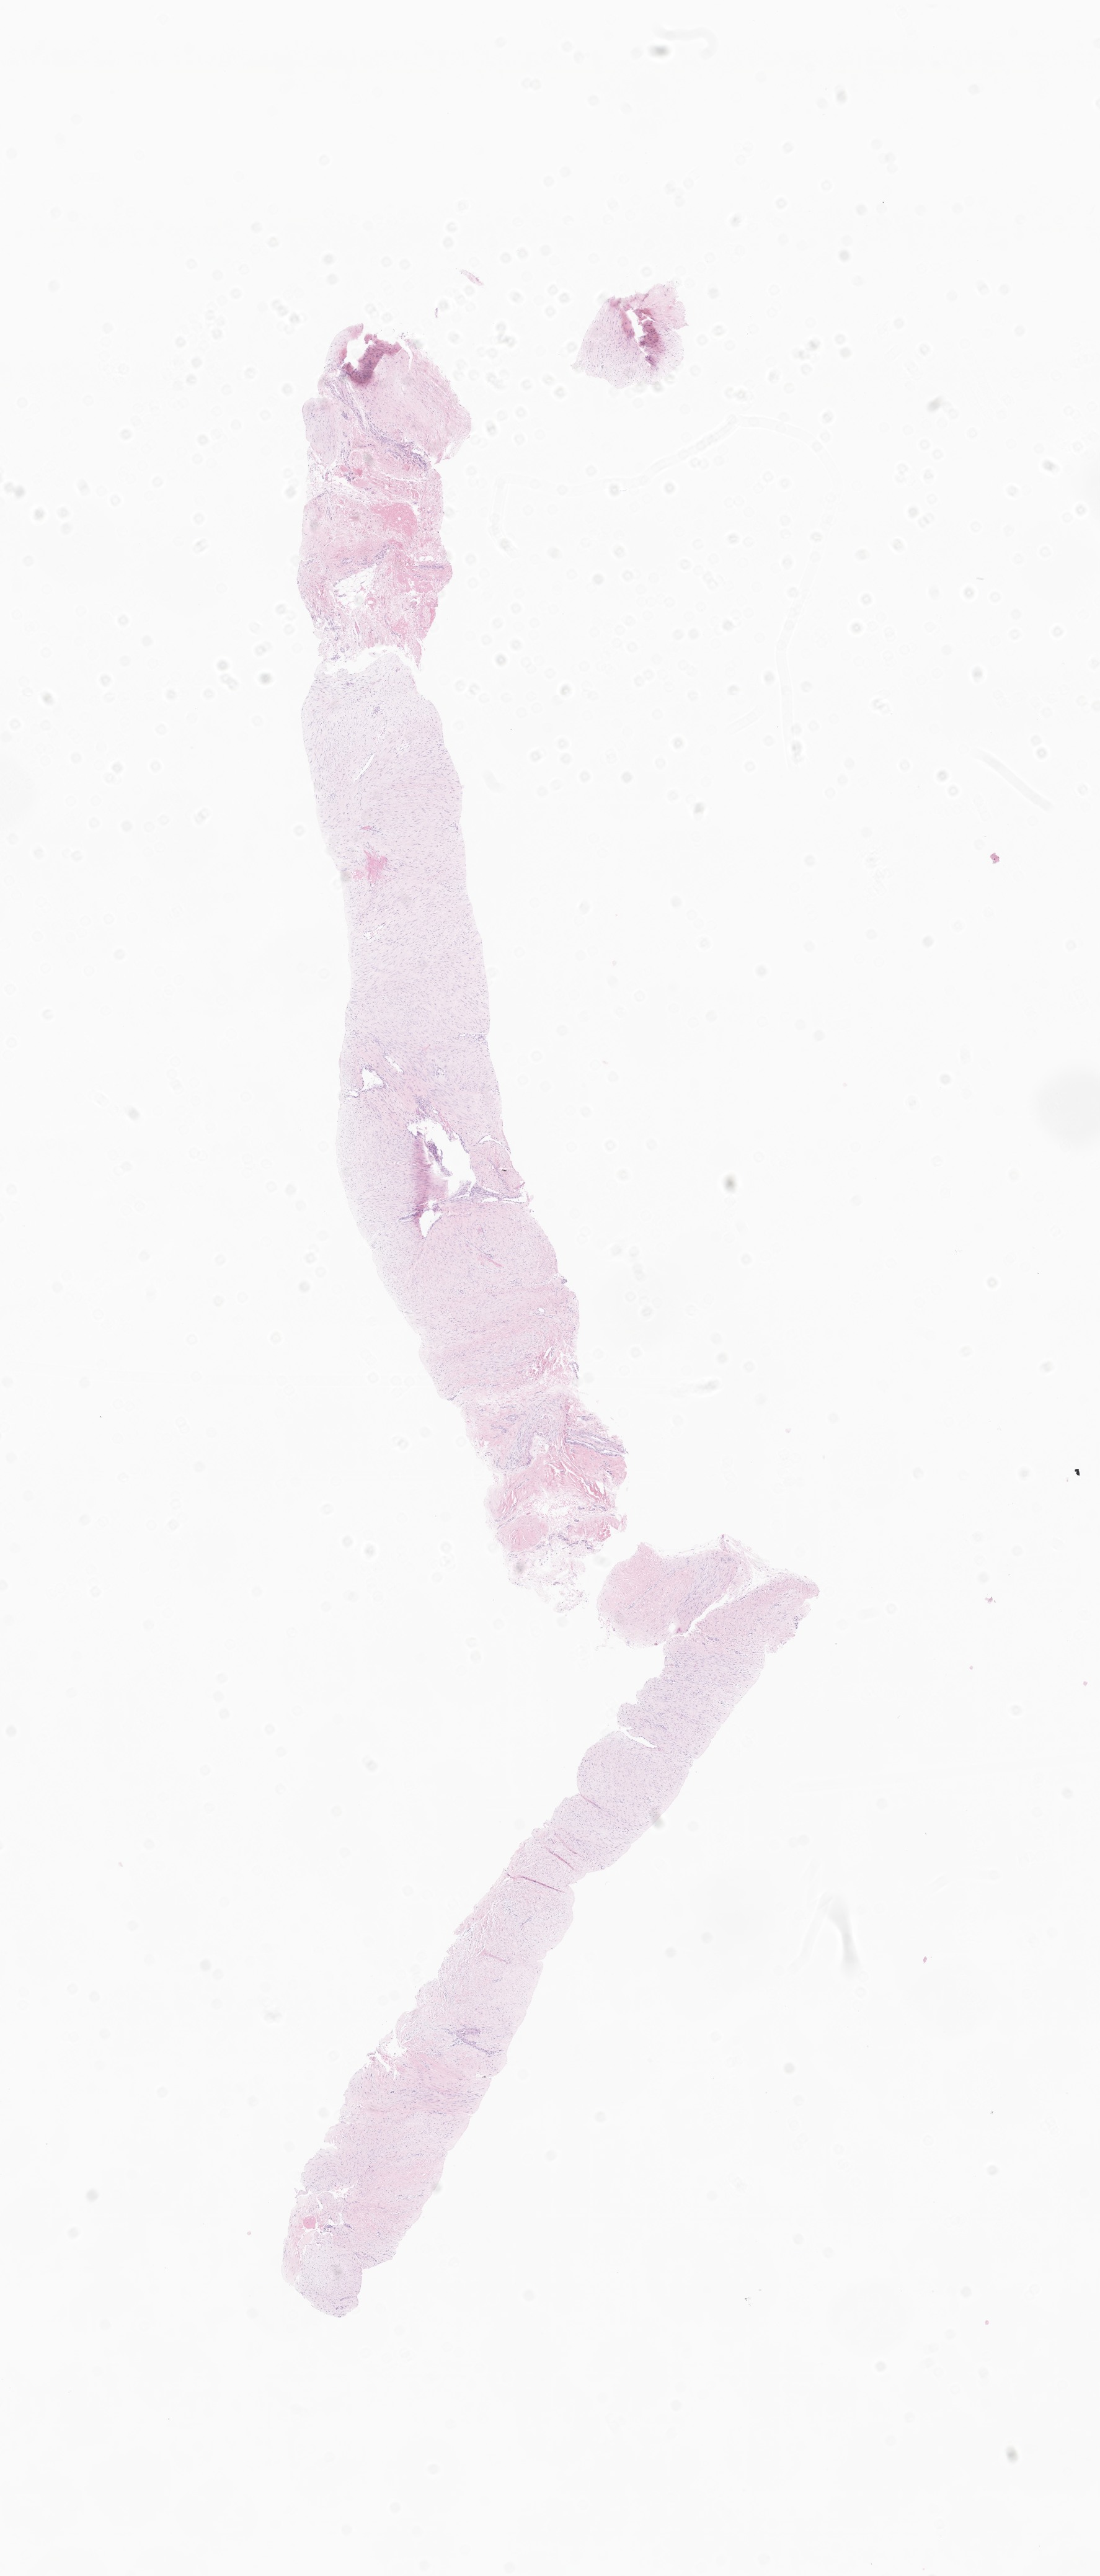
Digitized H&E-stained section of tumor tissue from the soft tissue of pelvis, low-resolution overview of the scanned area, about 7.5 x 17.5 mm, formalin-fixed, paraffin-embedded (FFPE) tissue. Patient: male, age 128 months (10 years 8 months).
Diagnosis: Aggressive fibromatosis.